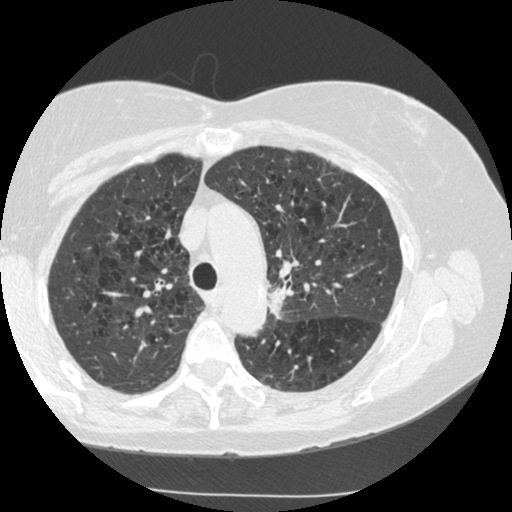
Axial slice from a low-dose chest CT screening exam. Second screening round (one year after baseline). Lung window (W 1500 / L -600 HU). 1.25 mm slice thickness. Standard (soft-tissue) reconstruction kernel (STANDARD). 120 kVp. Slice 187 of 249 in the series. 512 × 512 image matrix. Female participant, aged 70 years at enrolment.
Lesion marked by an expert reader, bounding box [x1, y1, x2, y2] px = [247, 267, 315, 329]. Screening reader's record for this exam (one nodule recorded; not confirmed to be the boxed lesion): non-calcified nodule or mass ≥4 mm, left upper lobe, 15 × 13 mm, spiculated (stellate) margins, soft tissue attenuation, pre-existing on the prior screen: yes; interval growth: yes. Official screen result: positive, other. Later outcome: lung cancer diagnosed 360 days after this screen (after the third annual screen) — neoplasm, malignant, left upper lobe, stage IIIB (AJCC 6th edition), 40 mm at pathology.